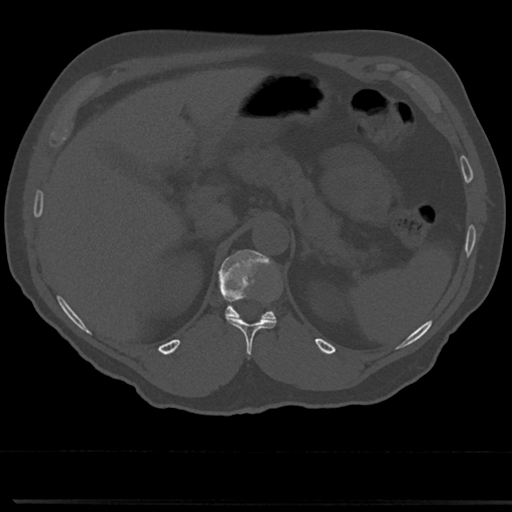
CT including the spine, one axial slice; slice 176 of 817 in the series (ordered by position); reconstruction kernel Br40s/3; bone window (W 1800 / L 400 HU); 0.5 mm slice thickness; 512 × 512 image matrix, field of view 355 × 355 mm. Patient: male, 61 years. From the clinical record (not read from this slice): primary cancer: prostate.
Annotated regions visible in this slice (semi-automatic segmentation, software-assisted and operator-edited):
- T11 vertebra: bounding box (x1, y1, x2, y2) in pixels: (227, 317, 276, 357)
- T12 vertebra: (217, 250, 279, 321)